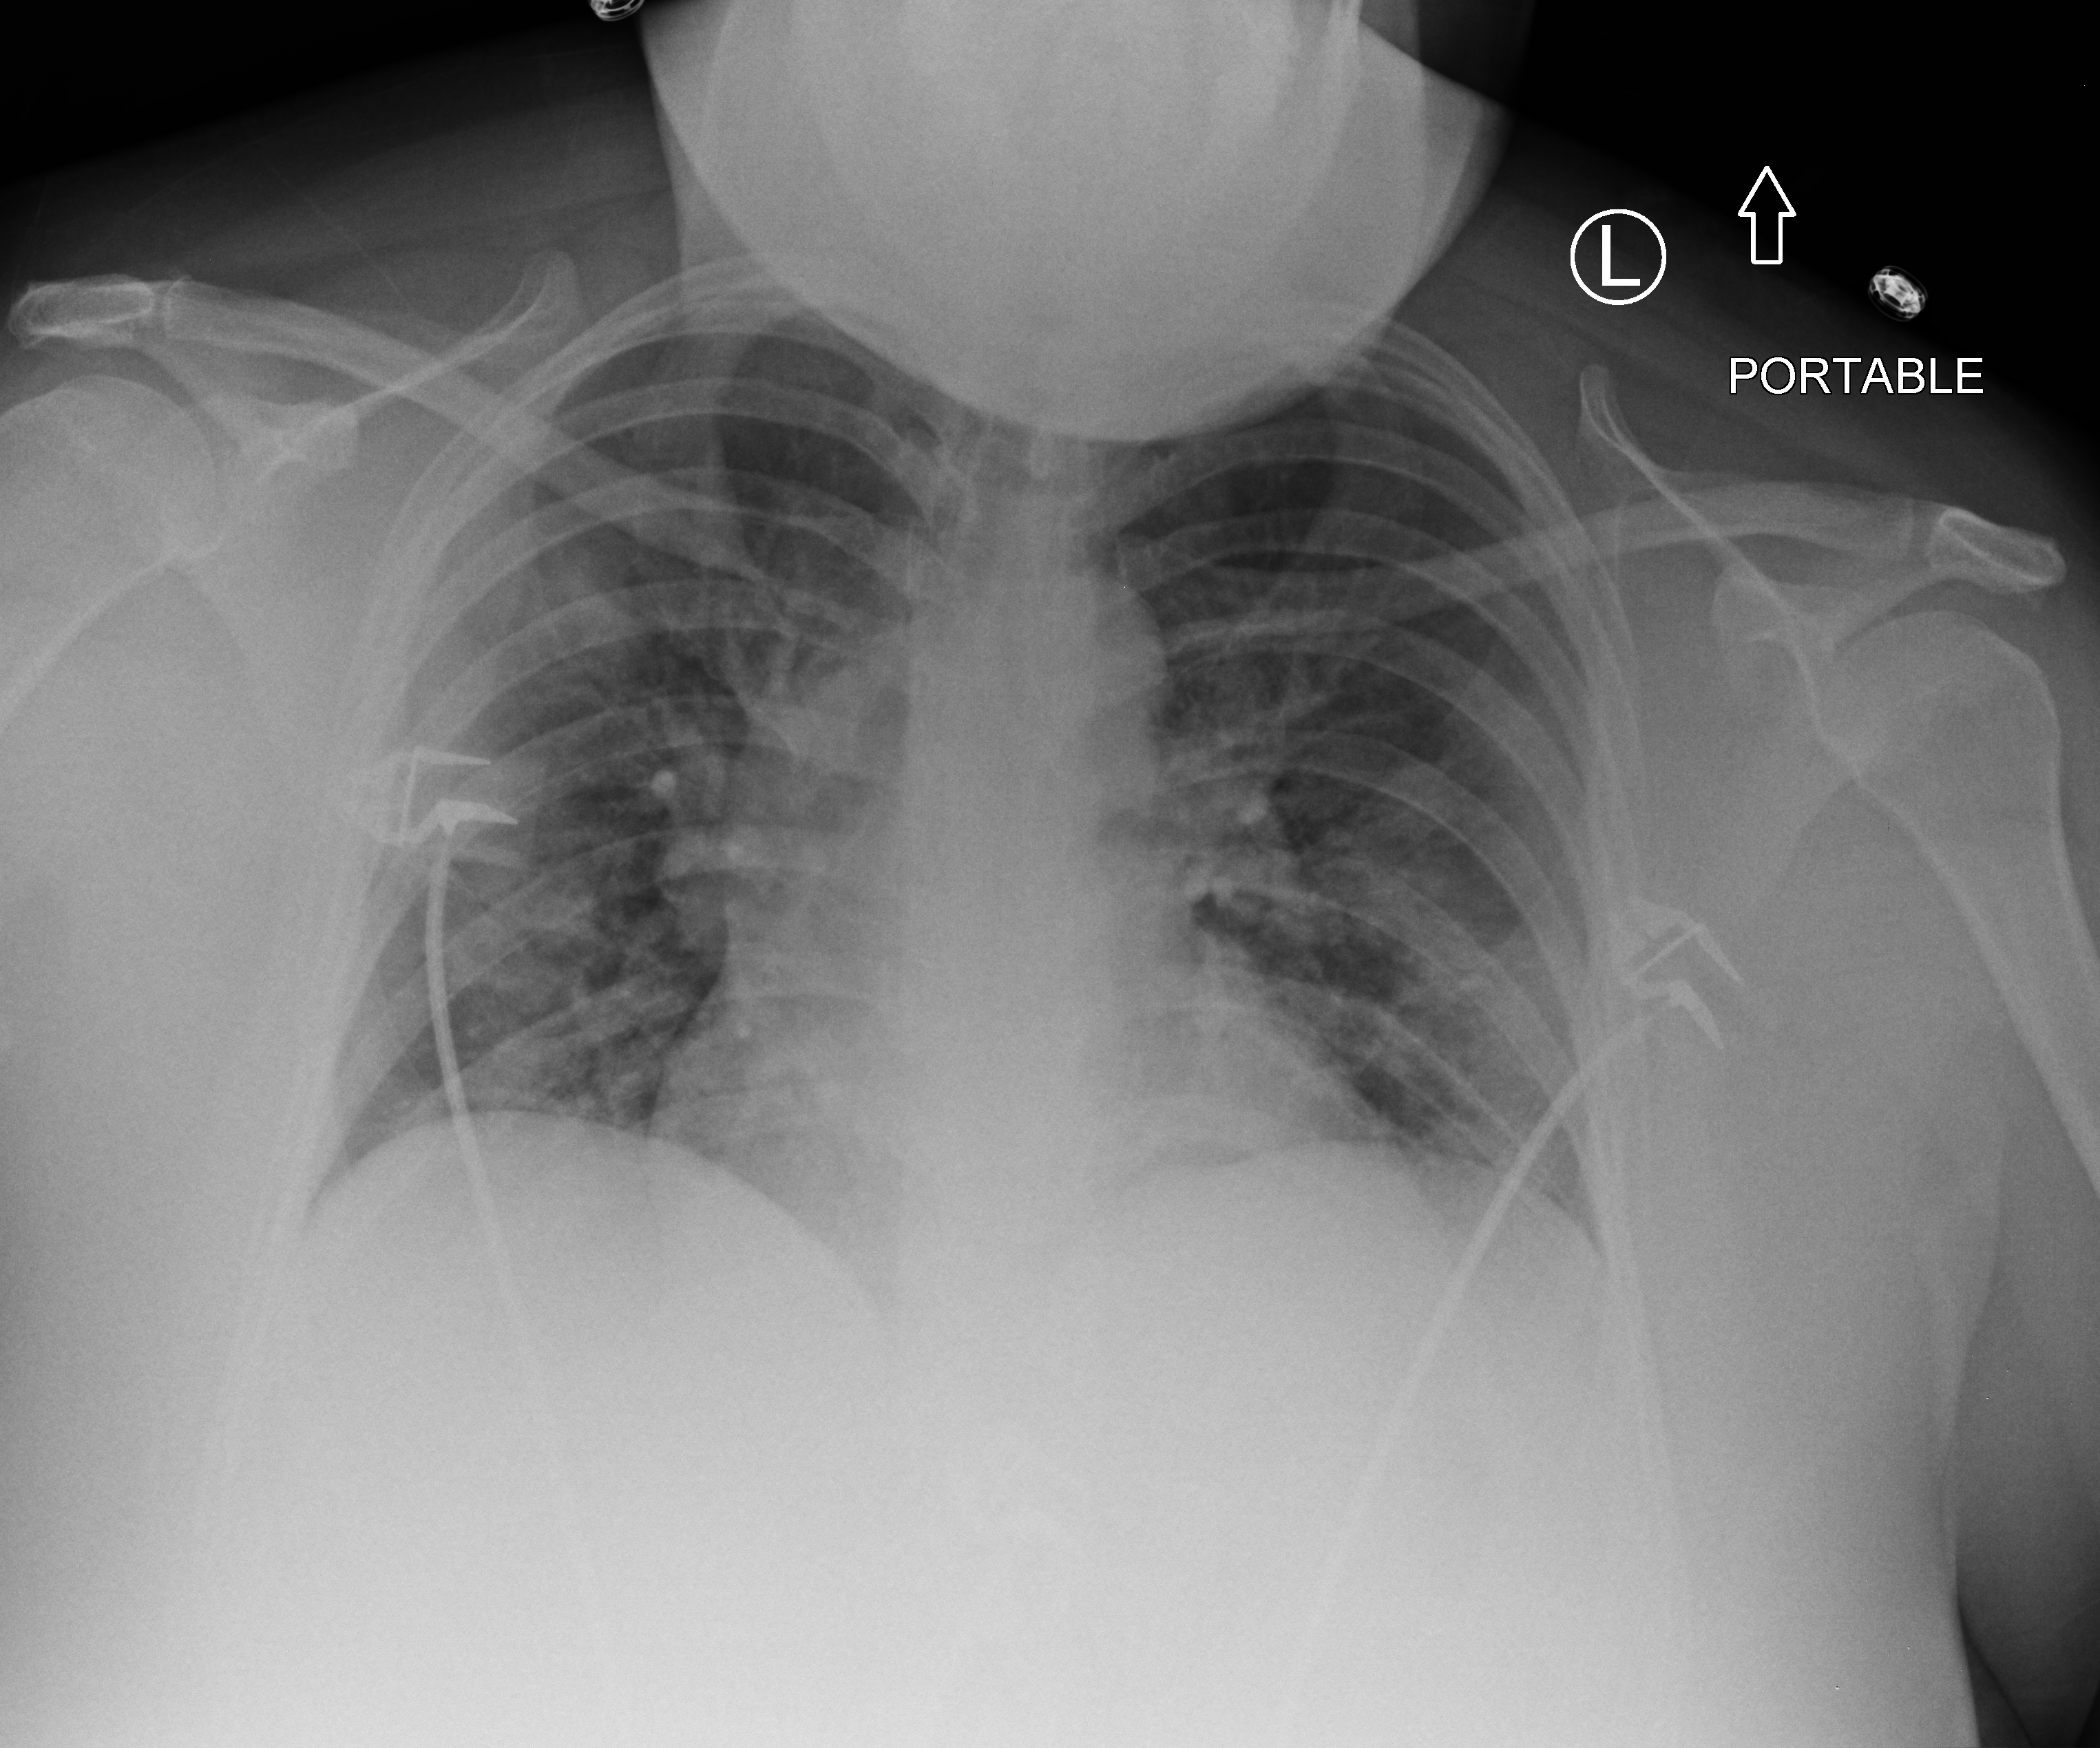
Bedside chest radiograph (computed radiography); anteroposterior (AP) projection. Patient hospitalised with COVID-19; female, aged 18–59 years.
Hospital-stay facts (about this admission, not read from this image; timing relative to this image not recorded): length of hospital stay: 10 days.